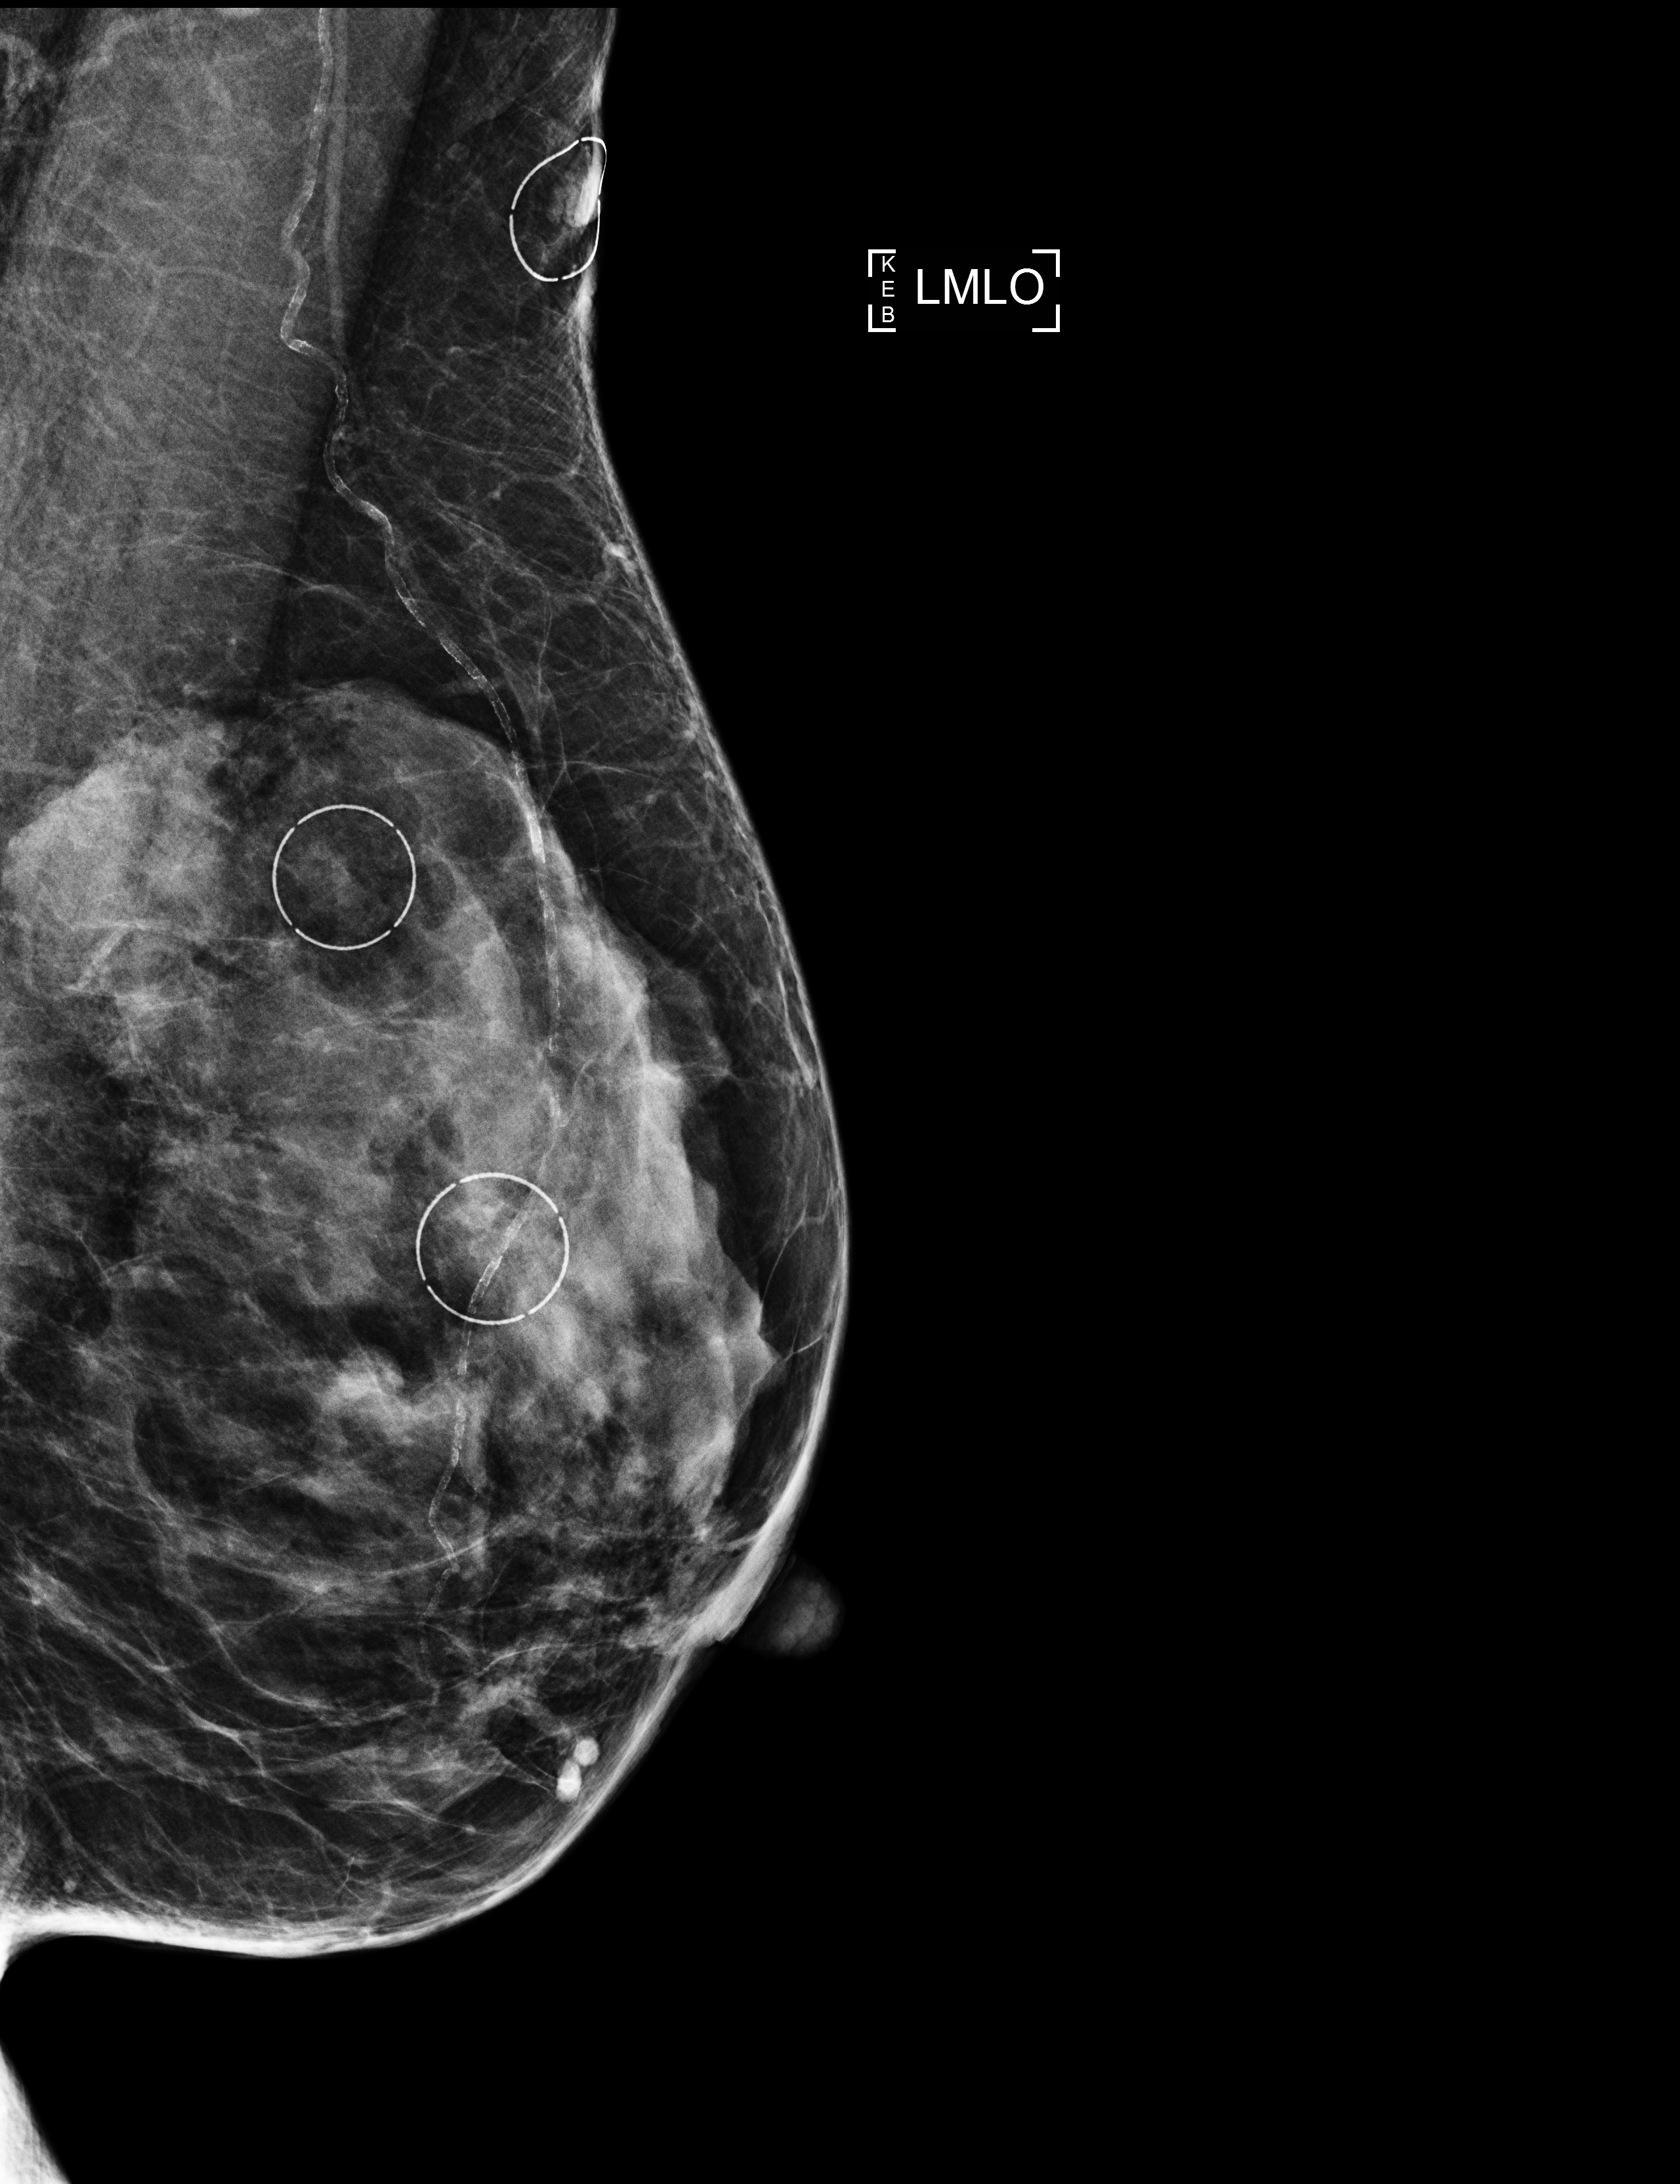
Annual screening mammography examination; compressed breast thickness 37 mm. Female patient, age 76 years.
Image type: full-field digital mammogram. Breast: left. Projection: mediolateral oblique (MLO) view.